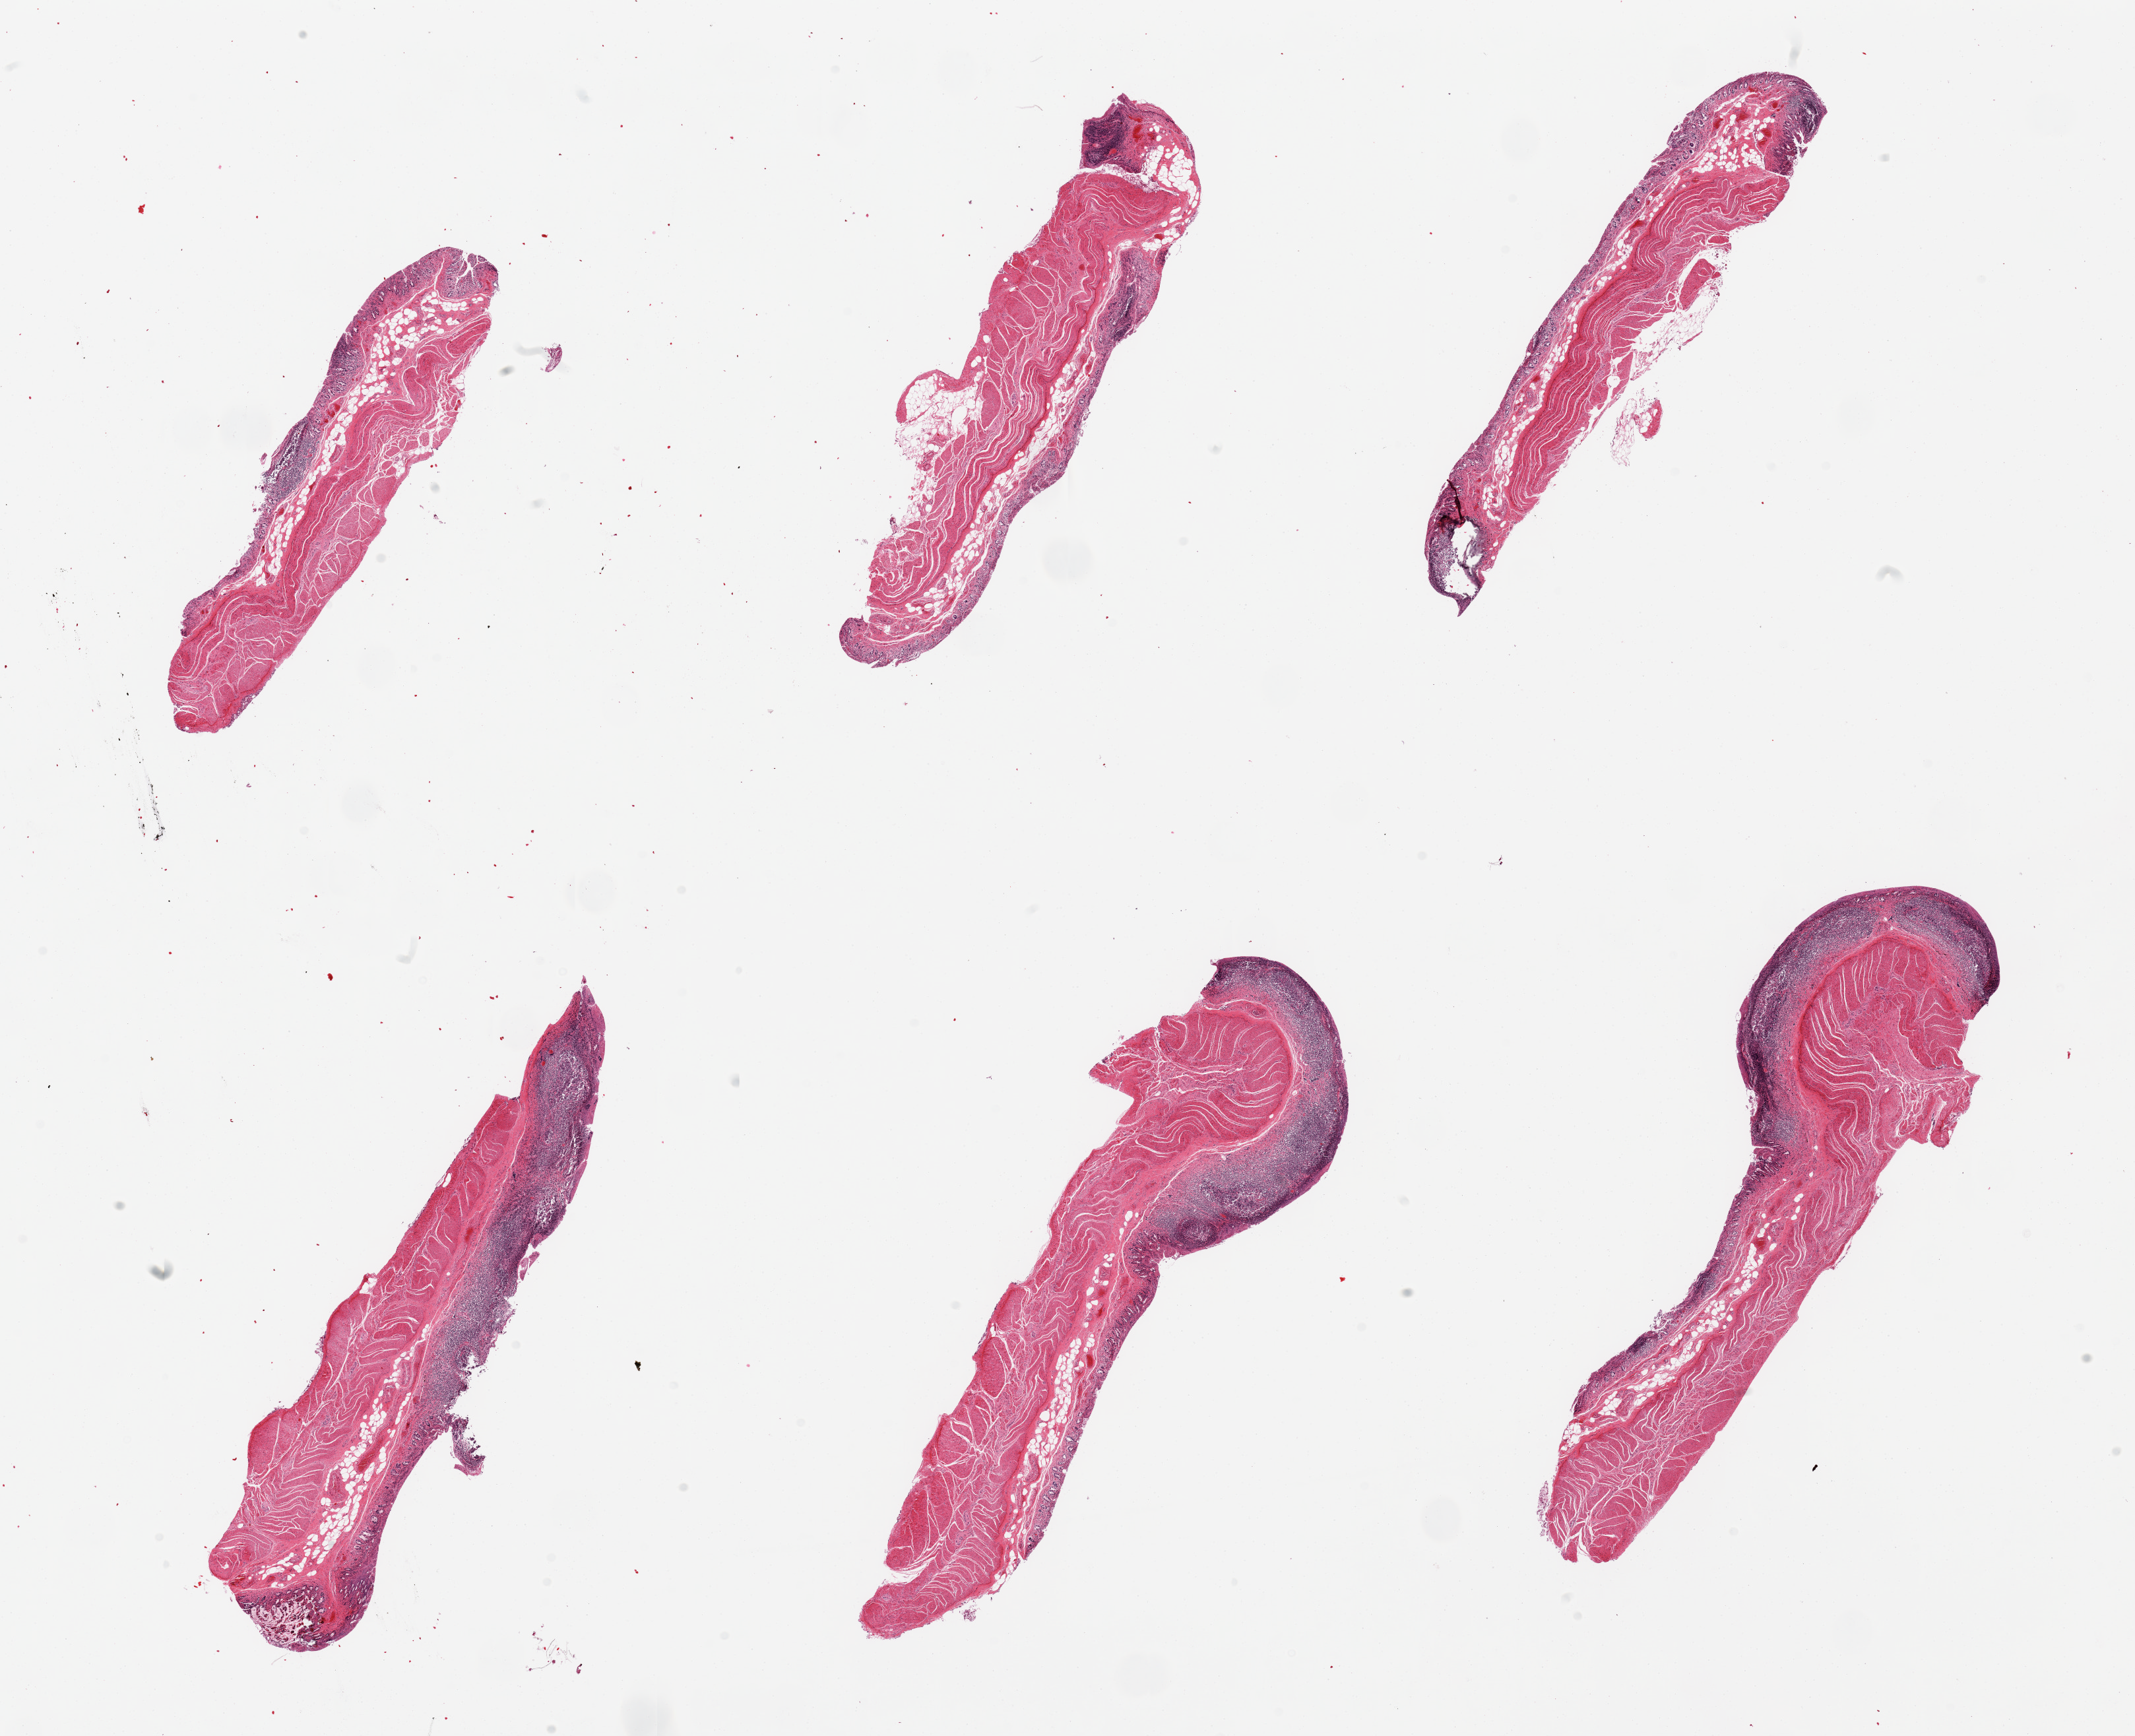
Whole-slide image, hematoxylin and eosin (H&E) stain — shown as a low-resolution overview of the whole scanned area (about 25.6 x 20.8 mm, from a 20x scan), PAXgene-fixed, paraffin-embedded tissue, section of ileum (target tissue), tissue donor sample. Donor: female.
Review note (as recorded): 6 pieces, mucosa autolyzed, ~15% residual lymphoid aggregates present.